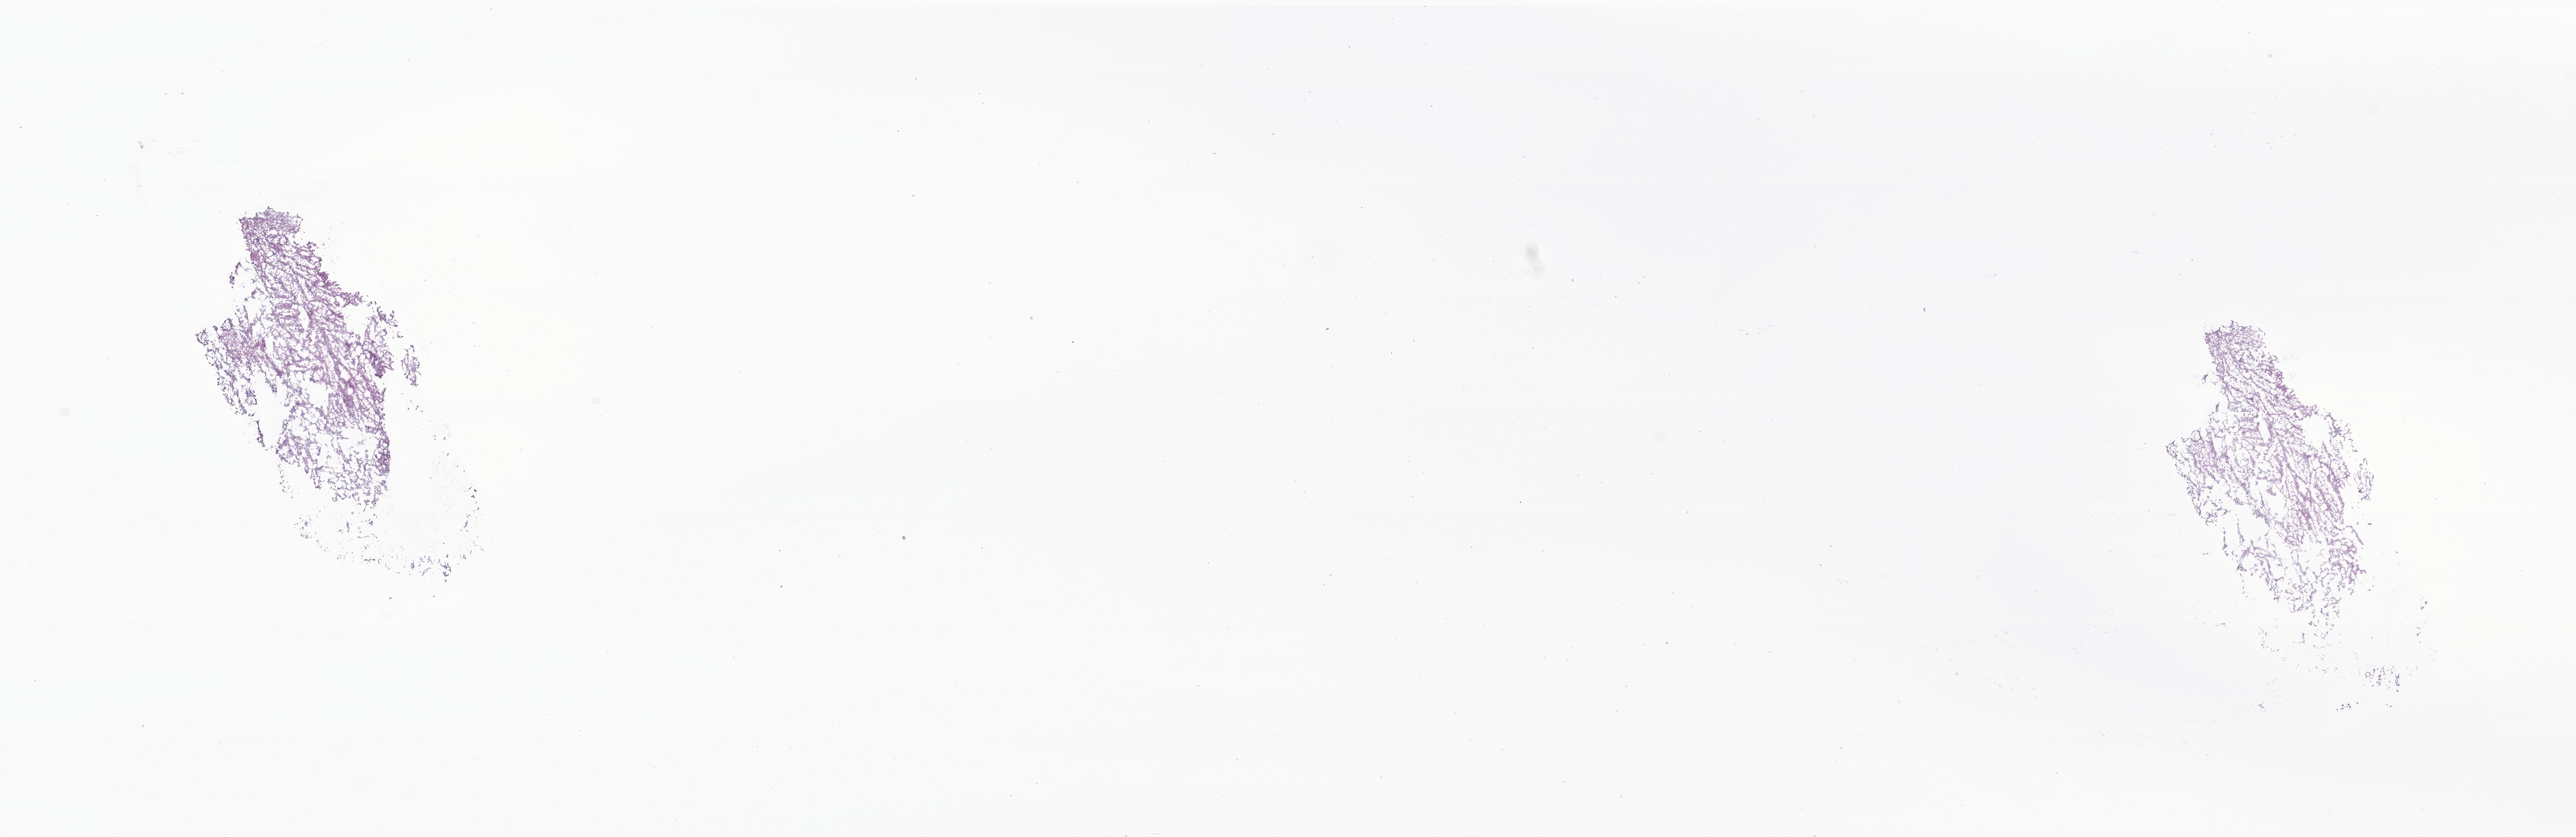
Digitized haematoxylin and eosin-stained section of tumor tissue from the brain, low-resolution overview of the scanned area, about 25.0 x 8.1 mm. Frozen section (OCT-embedded). Male patient, age 184 months (15 years 4 months).
Recorded diagnosis: Pilocytic astrocytoma.